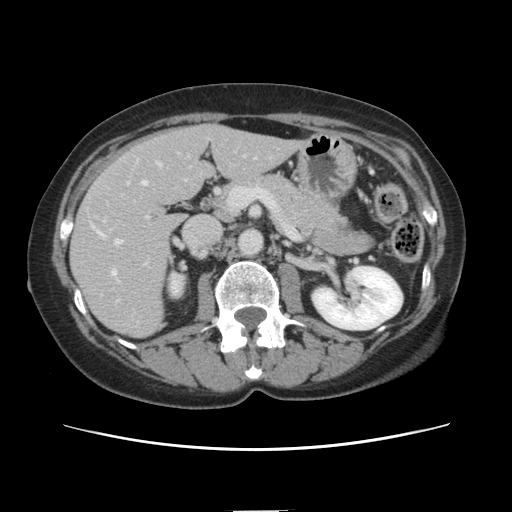
Contrast-enhanced abdominal CT, one axial slice; slice 63 of 141 in the series (ordered by position); 120 kVp; intravenous contrast given; soft-tissue window (W 400 / L 40 HU); 2.5 mm slice thickness; 512 × 512 image matrix, field of view 350 × 350 mm. Female patient, age 63 years. Case-level facts recorded for this patient, not image findings: diagnosis: colorectal cancer liver metastases, imaged before liver resection; multiple liver metastases: yes; largest metastasis: 3.2 cm.
Outlined on this slice (manually delineated by an expert):
- hepatic veins: box from (x=100, y=163) to (x=161, y=277) px
- liver: (x=72, y=125)–(x=299, y=337)
- planned liver remnant (the part of the liver to remain after resection): (x=176, y=125)–(x=299, y=189)
- portal vein (with intrahepatic branches): (x=95, y=180)–(x=145, y=229)